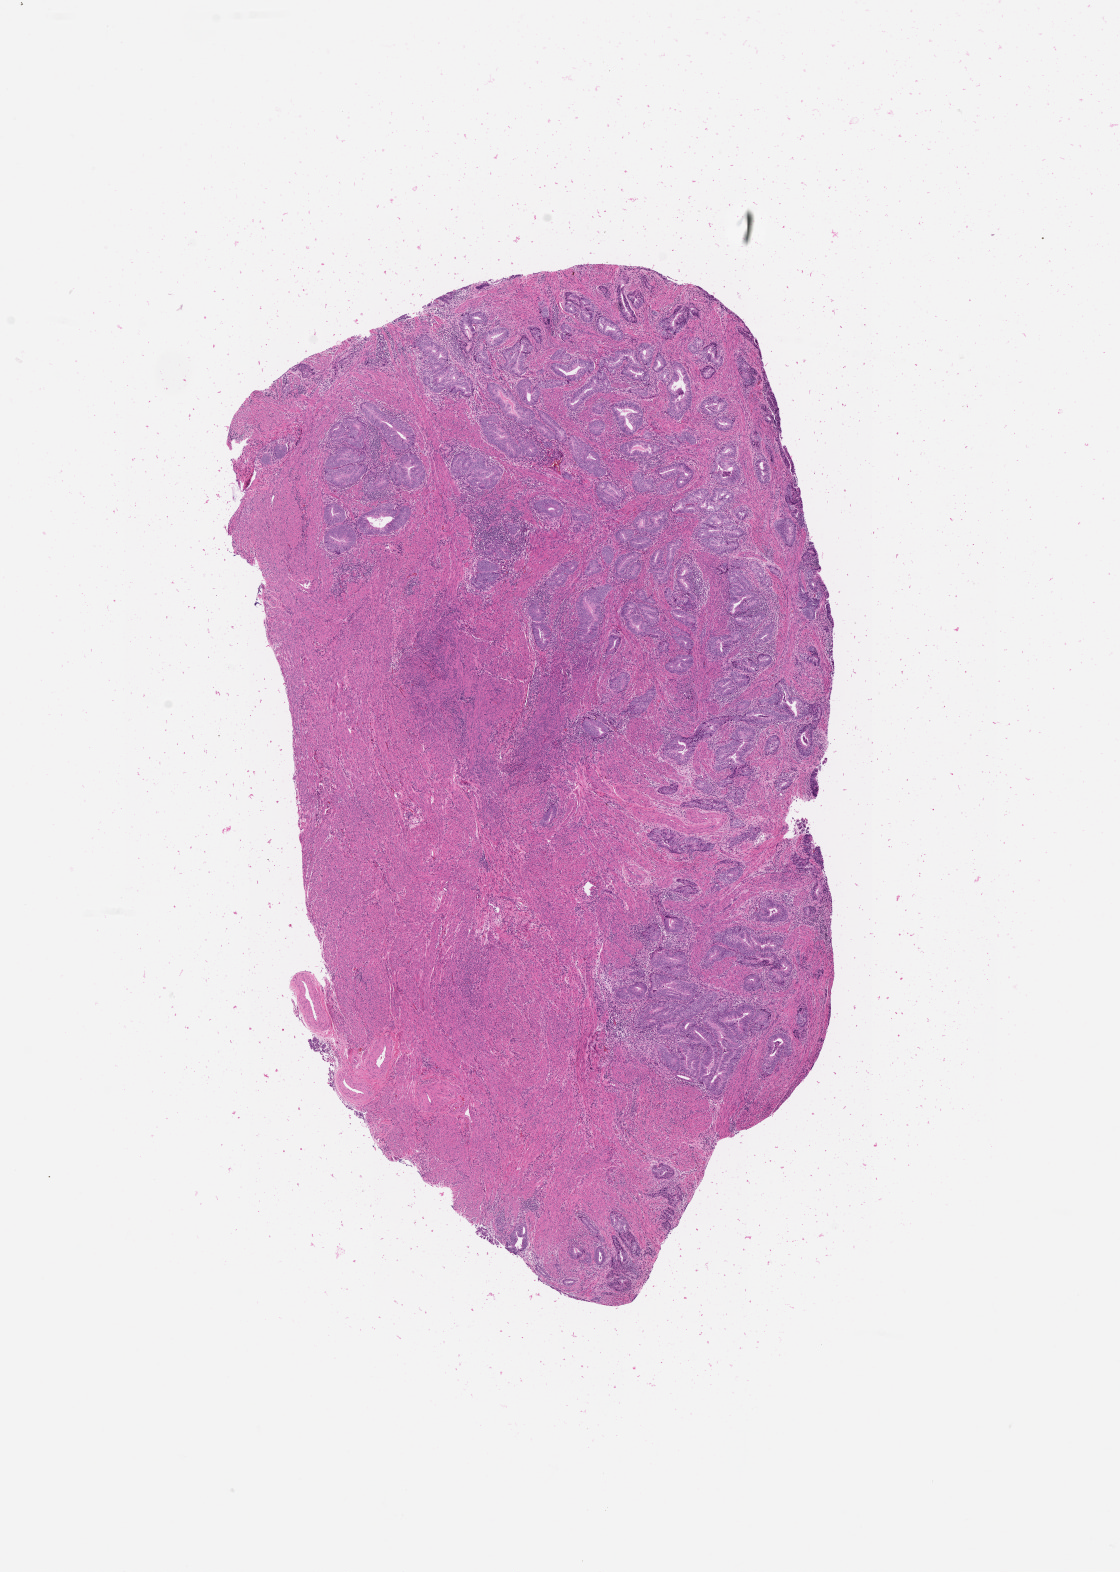
H&E whole-slide image, low-resolution overview of the scanned area, about 9.0 x 12.7 mm. Tumour tissue sample, uterus. 68-year-old female patient. Histologic grade: G2 (moderately differentiated).
Histologic diagnosis: Endometrioid adenocarcinoma, NOS.